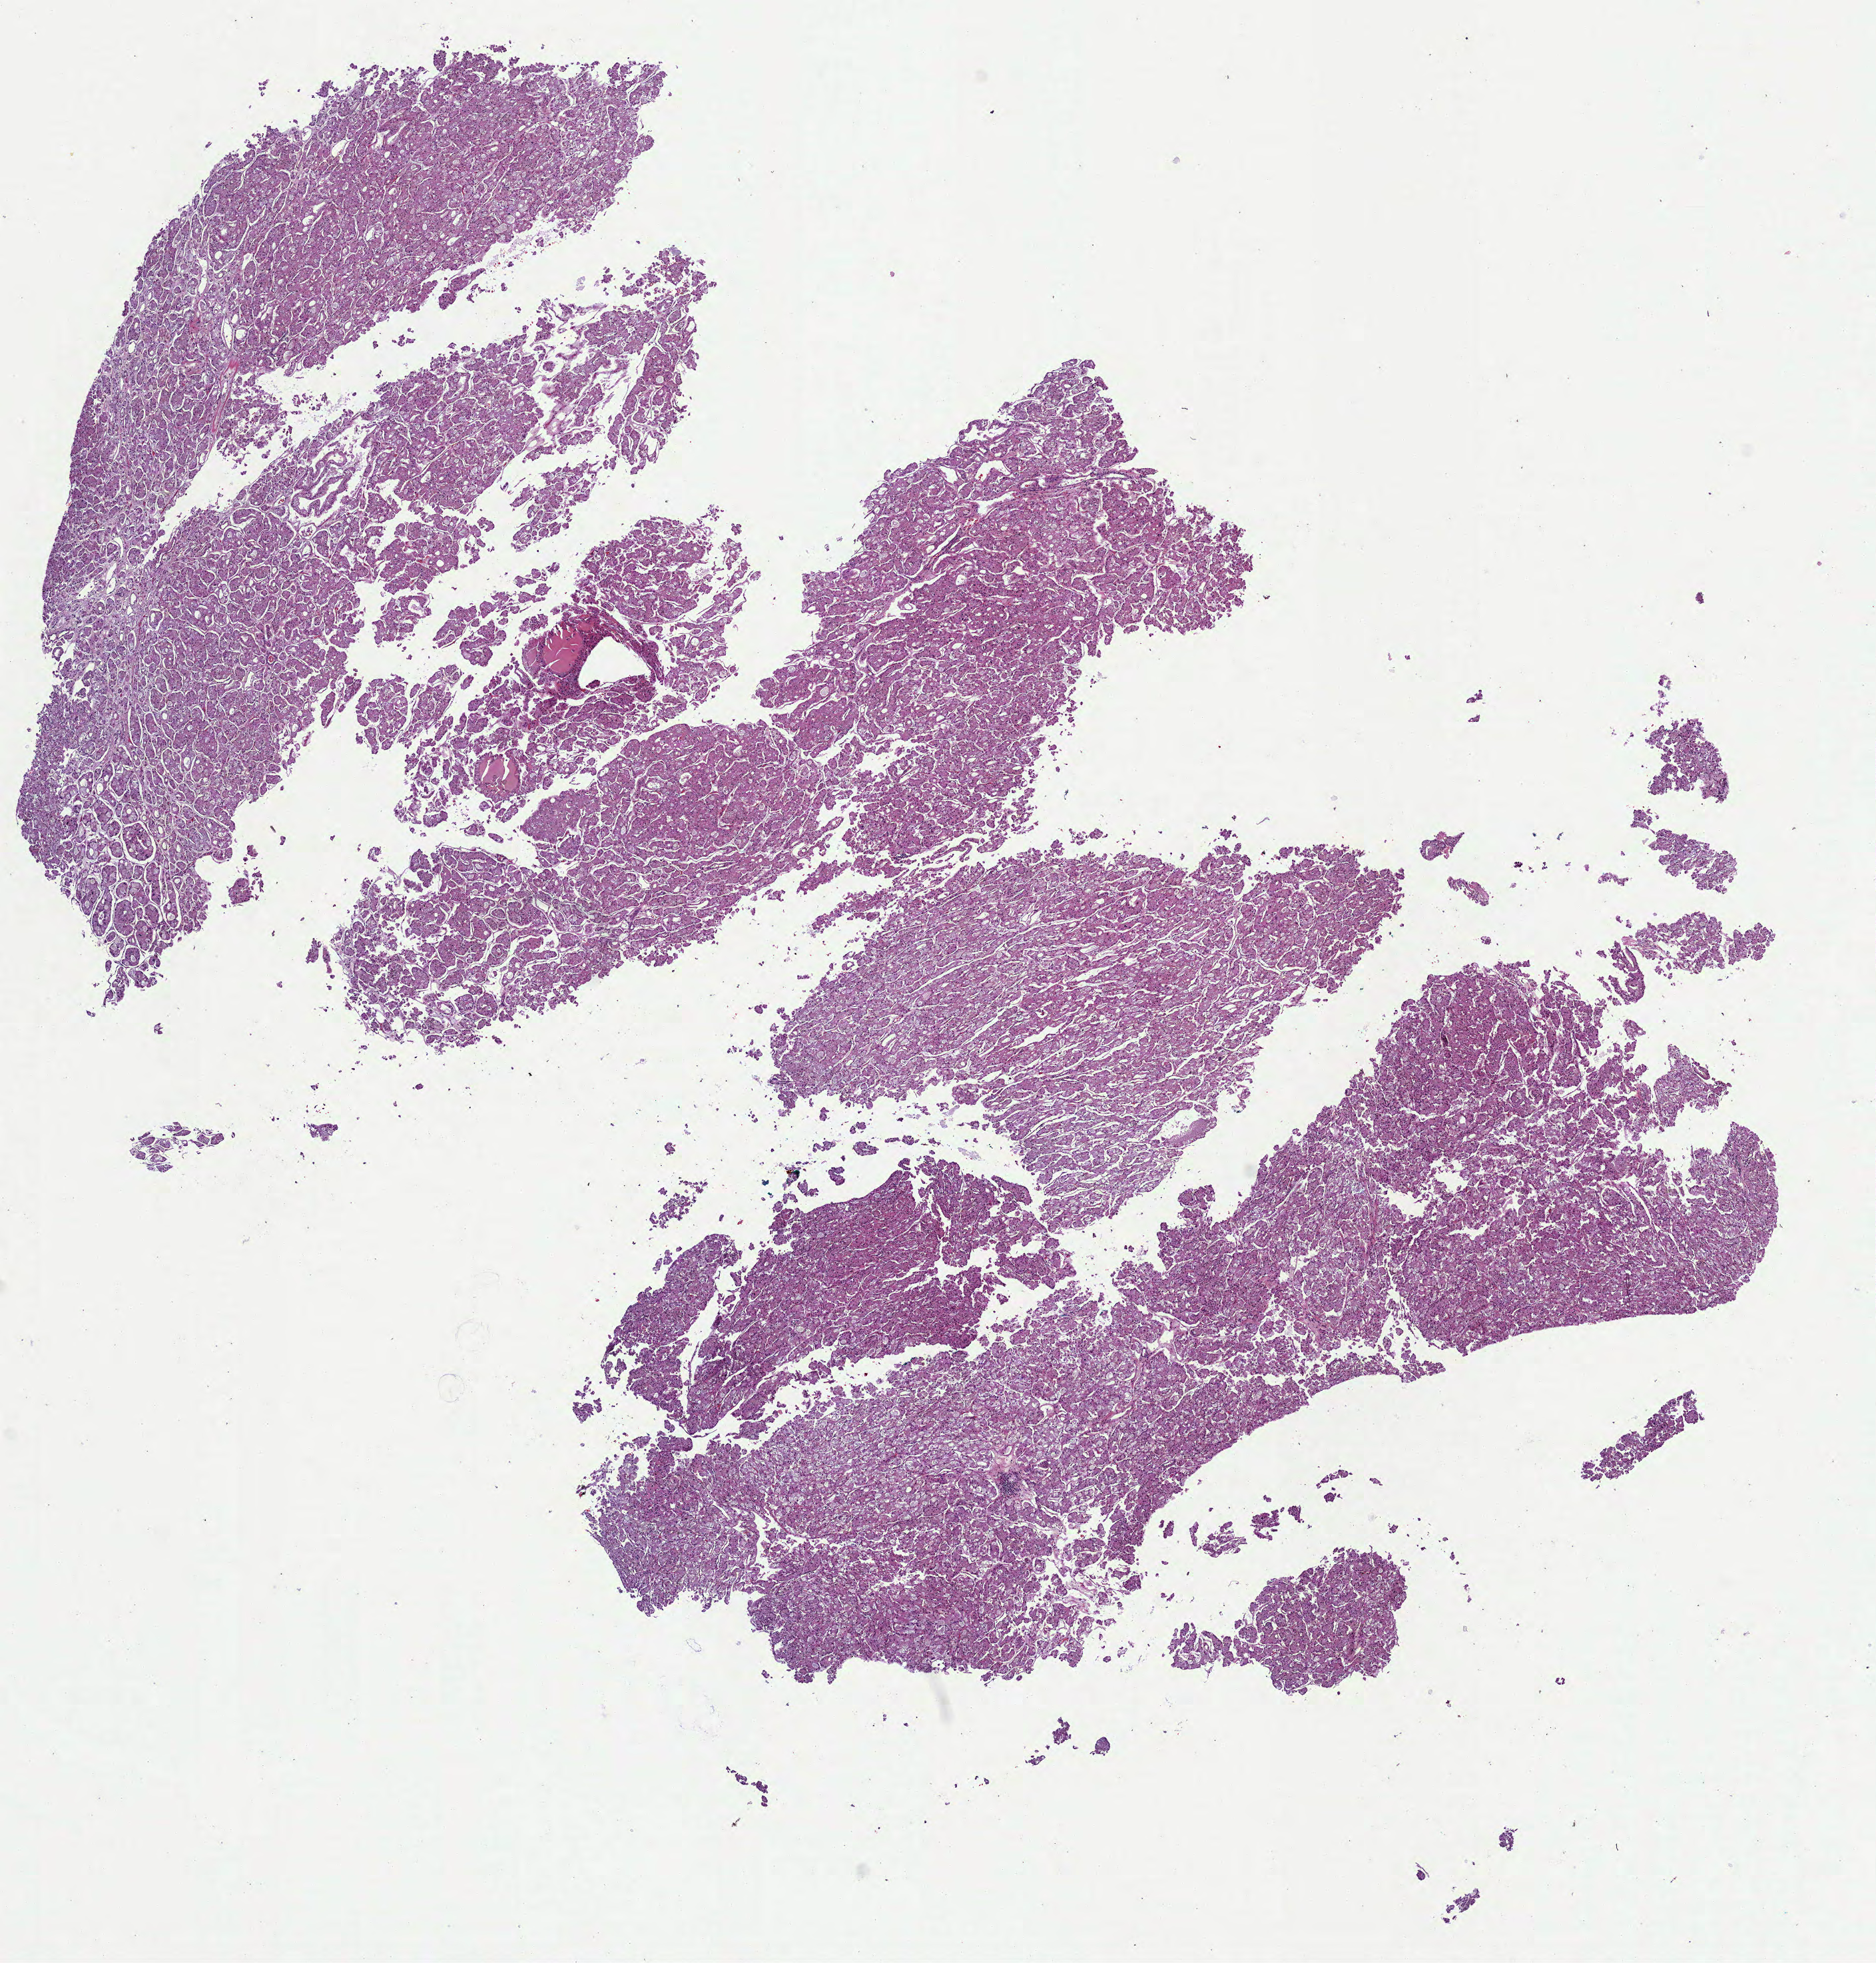
Whole-slide histology image, H&E — whole scanned area (about 11.4 x 11.9 mm, from a 40x scan) shown as a low-resolution overview, FFPE section, primary tumour sample from the kidney. Patient: female, age at initial diagnosis 66 years.
AJCC pathologic stage: I (7th edition). Diagnosis: Renal cell carcinoma, chromophobe type.